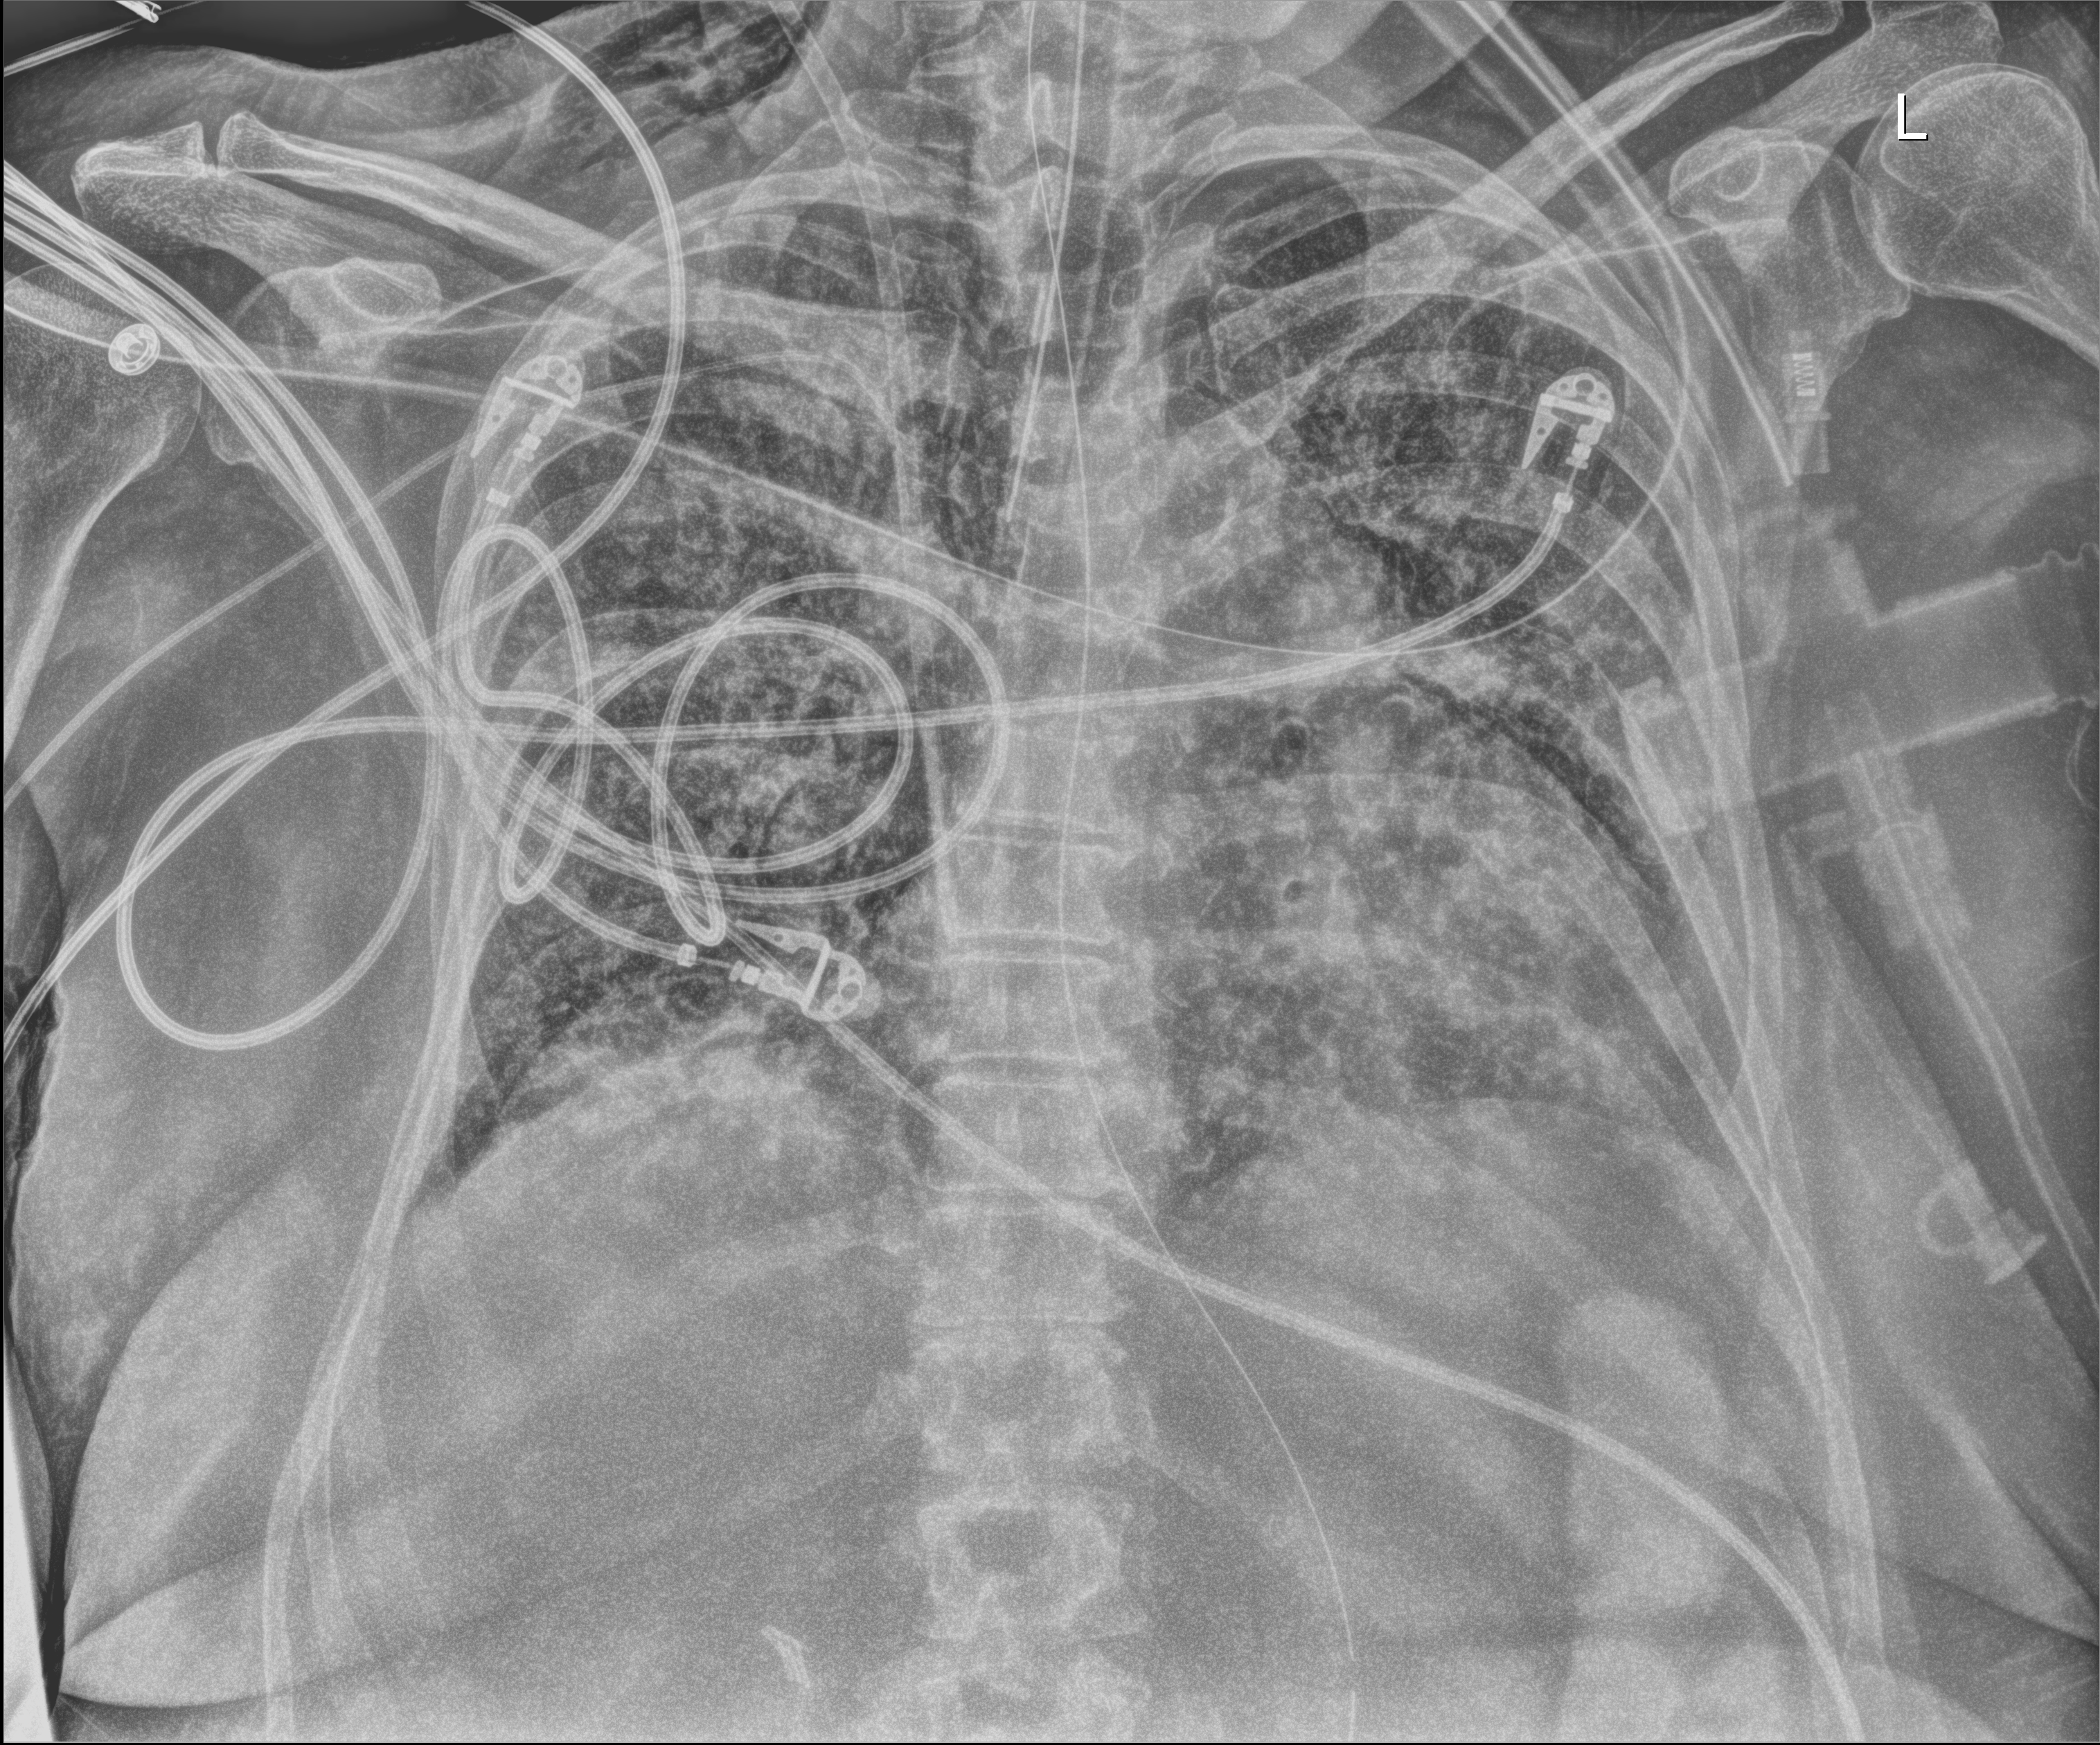
Chest radiograph, anteroposterior (AP) projection. Patient hospitalised with COVID-19; female, aged 60–74 years.
Hospital-stay facts (about this admission, not read from this image; timing relative to this image not recorded): mechanically ventilated during this hospital stay: yes.